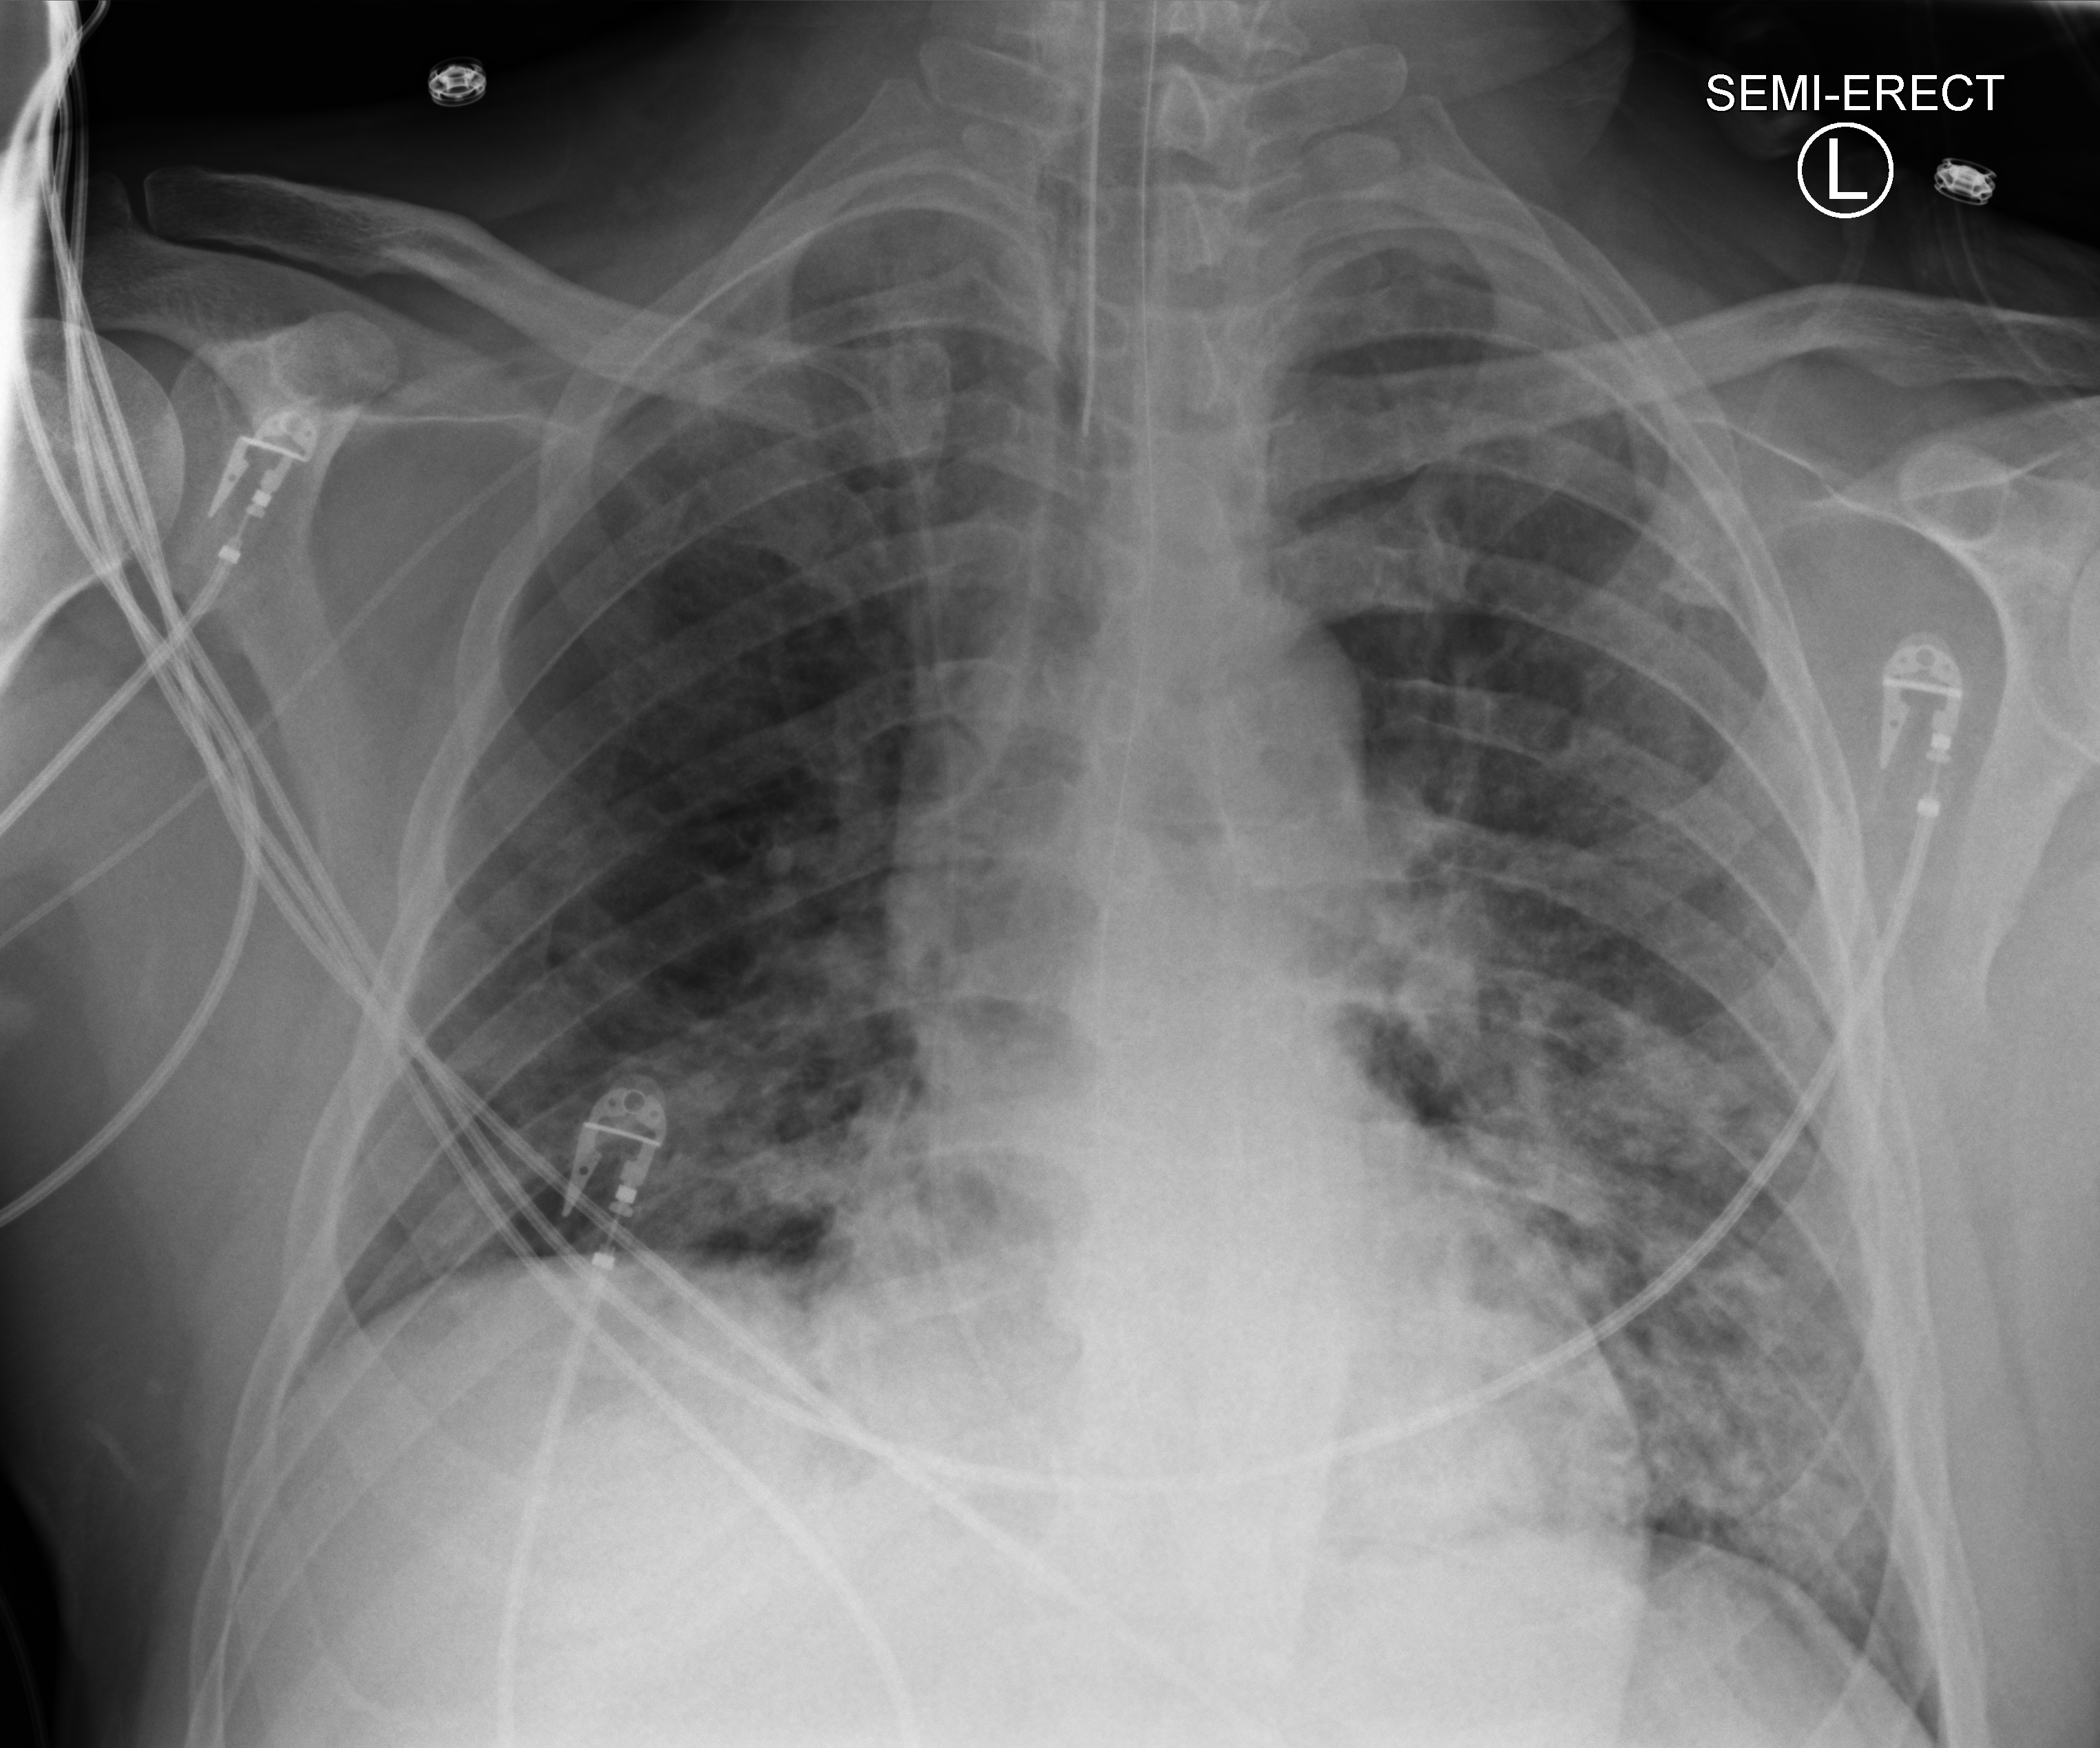
Chest X-ray (portable), anteroposterior (AP) projection. Male patient hospitalised with COVID-19, age 18–59 years.
Hospital-stay facts (about this admission, not read from this image; timing relative to this image not recorded): admitted to intensive care during this hospital stay: no.